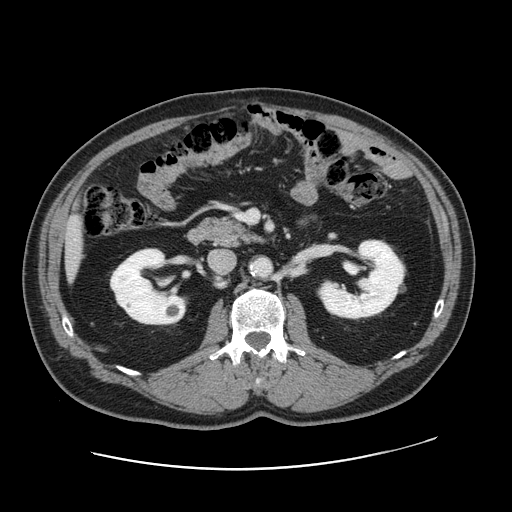
Contrast-enhanced abdominal CT, one axial slice. Slice 66 of 178 in the series (ordered by position). 120 kVp. Intravenous contrast given. Soft-tissue window (W 400 / L 40 HU). 2.5 mm slice thickness. 512 × 512 image matrix. Male patient, age 63 years. From the clinical record (not read from this slice): diagnosis: colorectal cancer liver metastases, imaged before liver resection; multiple liver metastases: yes; largest metastasis: 8 cm; disease in both lobes: yes.
Outlined on this slice (outlined manually by an expert reader):
- liver: bounding box <66,220,83,270> (left, top, right, bottom; pixels)